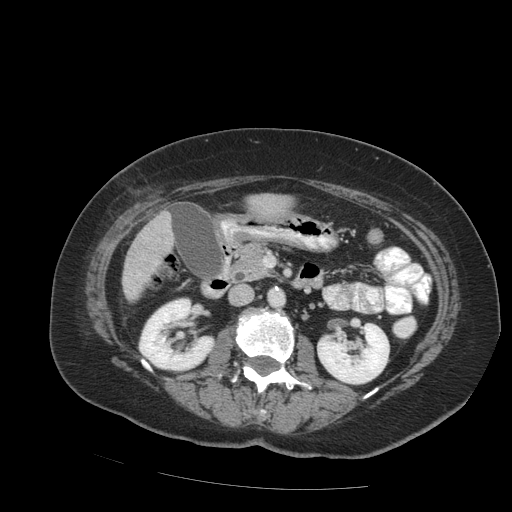
Contrast-enhanced abdominal CT (liver protocol), one axial slice; slice 30 of 99 in the series (ordered by position); soft-tissue window (W 400 / L 40 HU); 512 × 512 image matrix, field of view 400 × 400 mm. From the clinical record (not read from this slice): diagnosis: hepatocellular carcinoma (patient treated with transarterial chemoembolisation; whether this scan precedes or follows treatment is not stated here); TNM stage (as recorded): Stage-IVB; Child-Pugh class: A; tumour differentiation: moderately differentiated; tumour nodularity: uninodular.
Annotated regions visible in this slice (semi-automatically segmented with operator editing):
- liver parenchyma outside the tumour (the mass and vessels are separate outlines, so this box may not span the whole liver): bounding box [x1, y1, x2, y2] px = [122, 212, 172, 300]